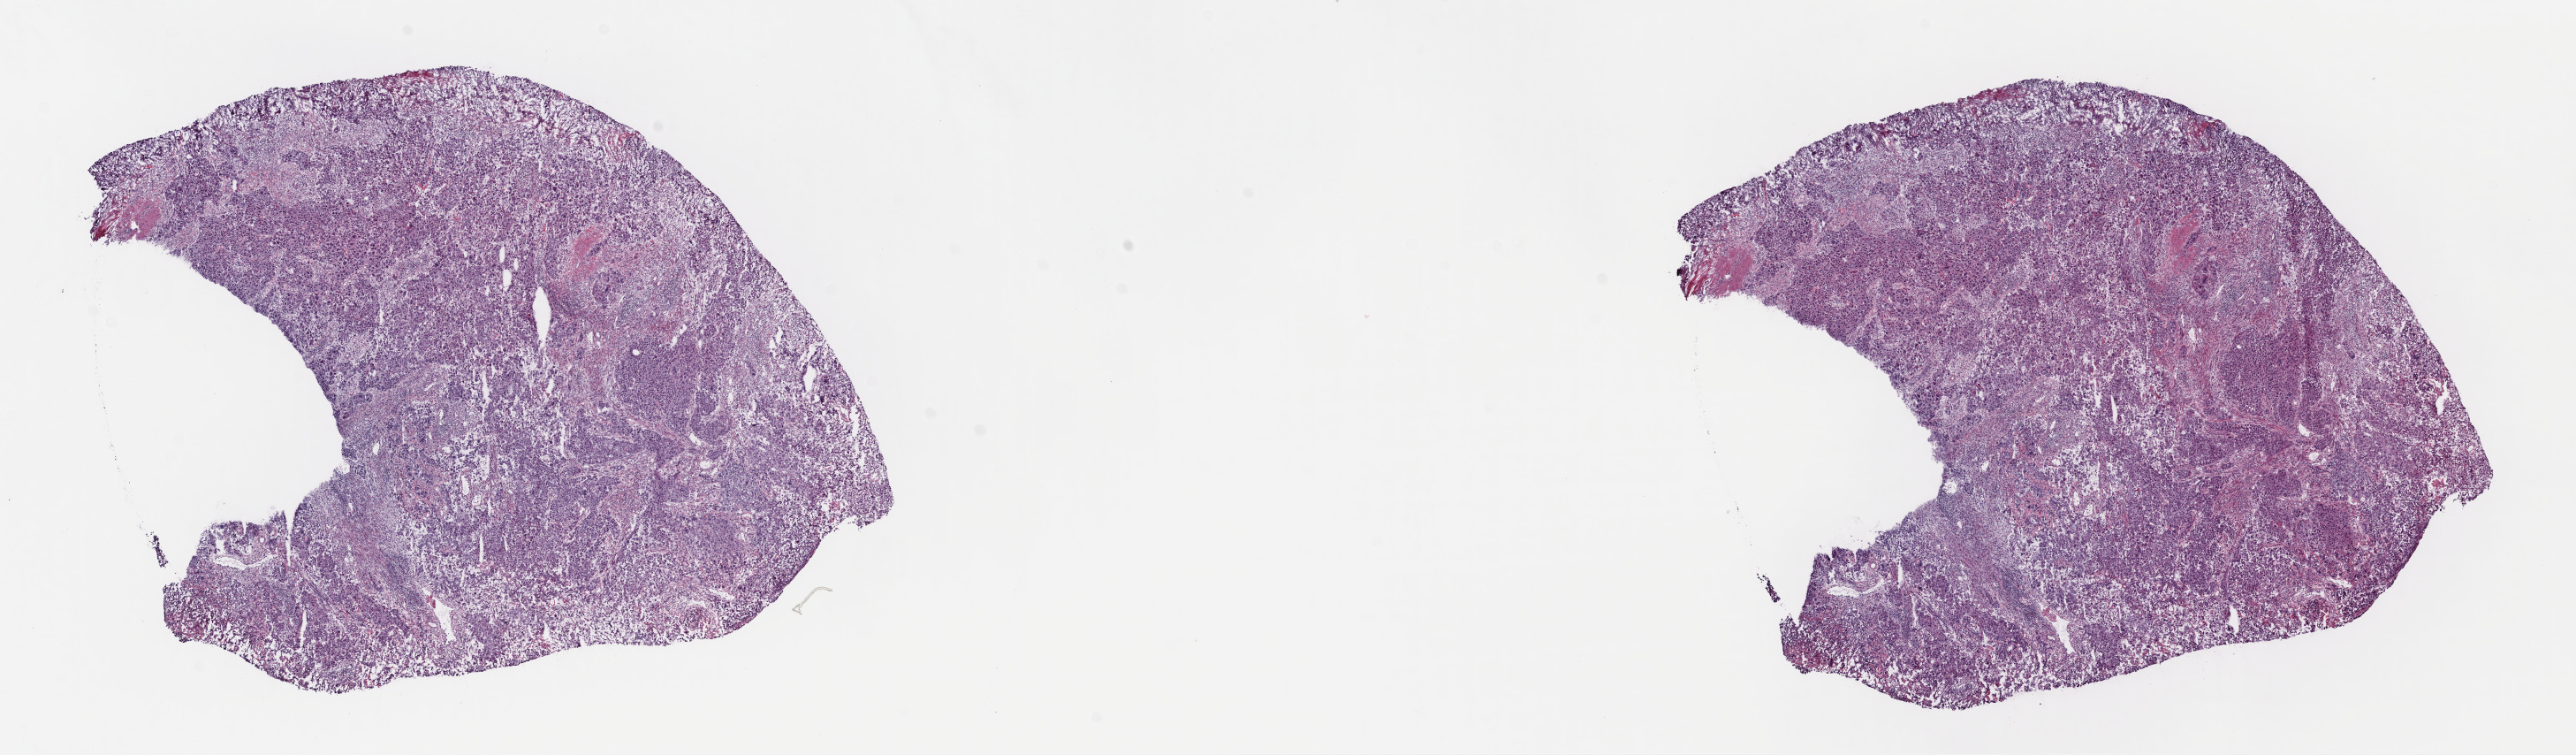
Digitized H&E tissue section (whole slide) — a low-resolution overview of the entire scanned area, about 22.9 x 6.7 mm (slide scanned at 40x), frozen section from the top of the tissue portion, bladder, primary tumour sample. Patient: male, age at initial diagnosis 70 years. Histologic grade: high grade. Pathologist review of this section (percent, as recorded): tumour cells 80%, tumour nuclei 85%, normal cells 0%, stromal cells 15%, necrosis 5%. Infiltration values recorded for this section: lymphocyte infiltration 0%, monocyte infiltration 0%, neutrophil infiltration 0%.
Lymph nodes positive (case pathology): 0 of 8 examined. AJCC pathologic stage: III (7th edition). Diagnosis: Transitional cell carcinoma.